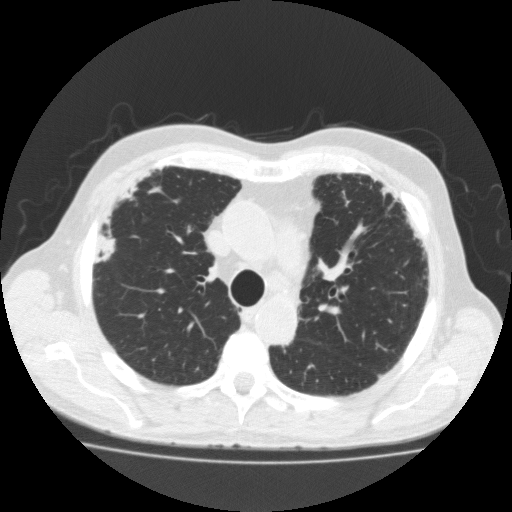
Low-dose screening chest CT, one axial slice; position 132 of 188 along the scan axis; 120 kVp; lung window (W 1500 / L -600 HU); 2 mm slice thickness; 512 × 512 image matrix.
Structures marked on this image (manually delineated by an expert):
- lesion 1 (tumor, upper lobe of right lung): box from (x=101, y=238) to (x=115, y=253) px